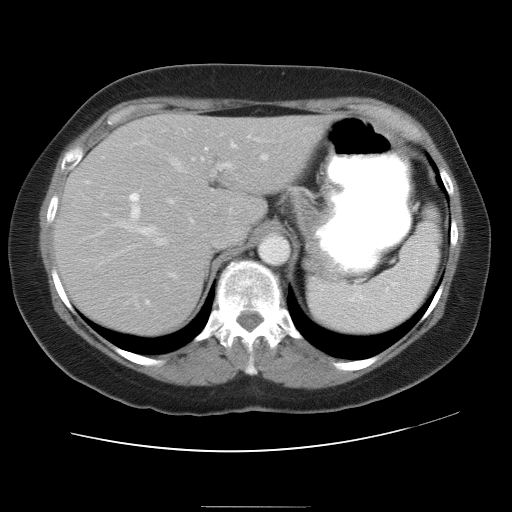
Contrast-enhanced abdominal CT, one axial slice; position 23 of 30 along the scan axis; reconstruction kernel STANDARD; 120 kVp; intravenous contrast given; soft-tissue window (W 400 / L 40 HU); 7.5 mm slice thickness; 512 × 512 image matrix, field of view 376 × 376 mm. Female patient, age 52 years. Case-level facts recorded for this patient, not image findings: diagnosis: colorectal cancer liver metastases, imaged before liver resection; multiple liver metastases: no.
Structures marked on this image (expert manual segmentation):
- hepatic veins: box from (x=82, y=155) to (x=267, y=266) px
- liver: (x=54, y=114)–(x=329, y=337)
- planned liver remnant (the part of the liver to remain after resection): (x=149, y=114)–(x=329, y=222)
- portal vein (with intrahepatic branches): (x=124, y=134)–(x=260, y=305)